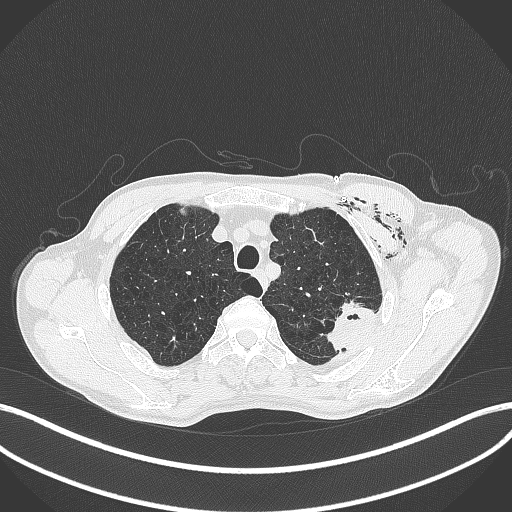
Chest CT, one axial slice. Slice 341 of 457 in the series (ordered by position). 120 kVp. Lung window (W 1500 / L -600 HU). 512 × 512 image matrix, field of view 400 × 400 mm. Patient: male, 58 years. Case-level facts recorded for this patient, not image findings: clinical TNM (as recorded): T3 N0 M0.
Annotated regions visible in this slice (bounding box drawn by a radiologist):
- lung tumour (recorded histology: adenocarcinoma): bounding box [x1, y1, x2, y2] px = [319, 298, 384, 353]